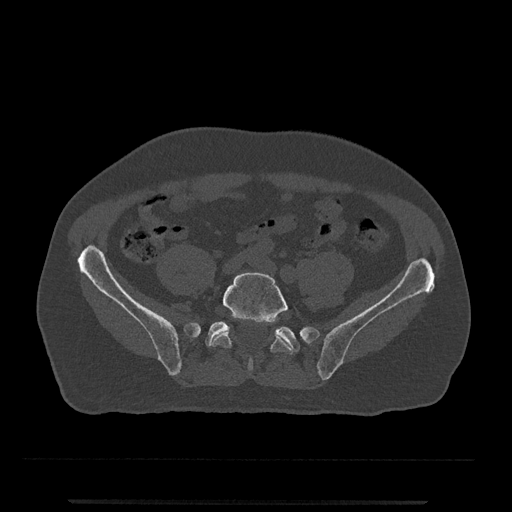
CT including the spine, one axial slice; reconstruction kernel Br40s/3; bone window (W 1800 / L 400 HU); 512 × 512 image matrix, field of view 419 × 419 mm. Patient: male, 63 years. Case-level facts recorded for this patient, not image findings: primary cancer: prostate.
Outlined on this slice (semi-automatically segmented with operator editing):
- L5 vertebra: box from (x=210, y=272) to (x=292, y=371) px